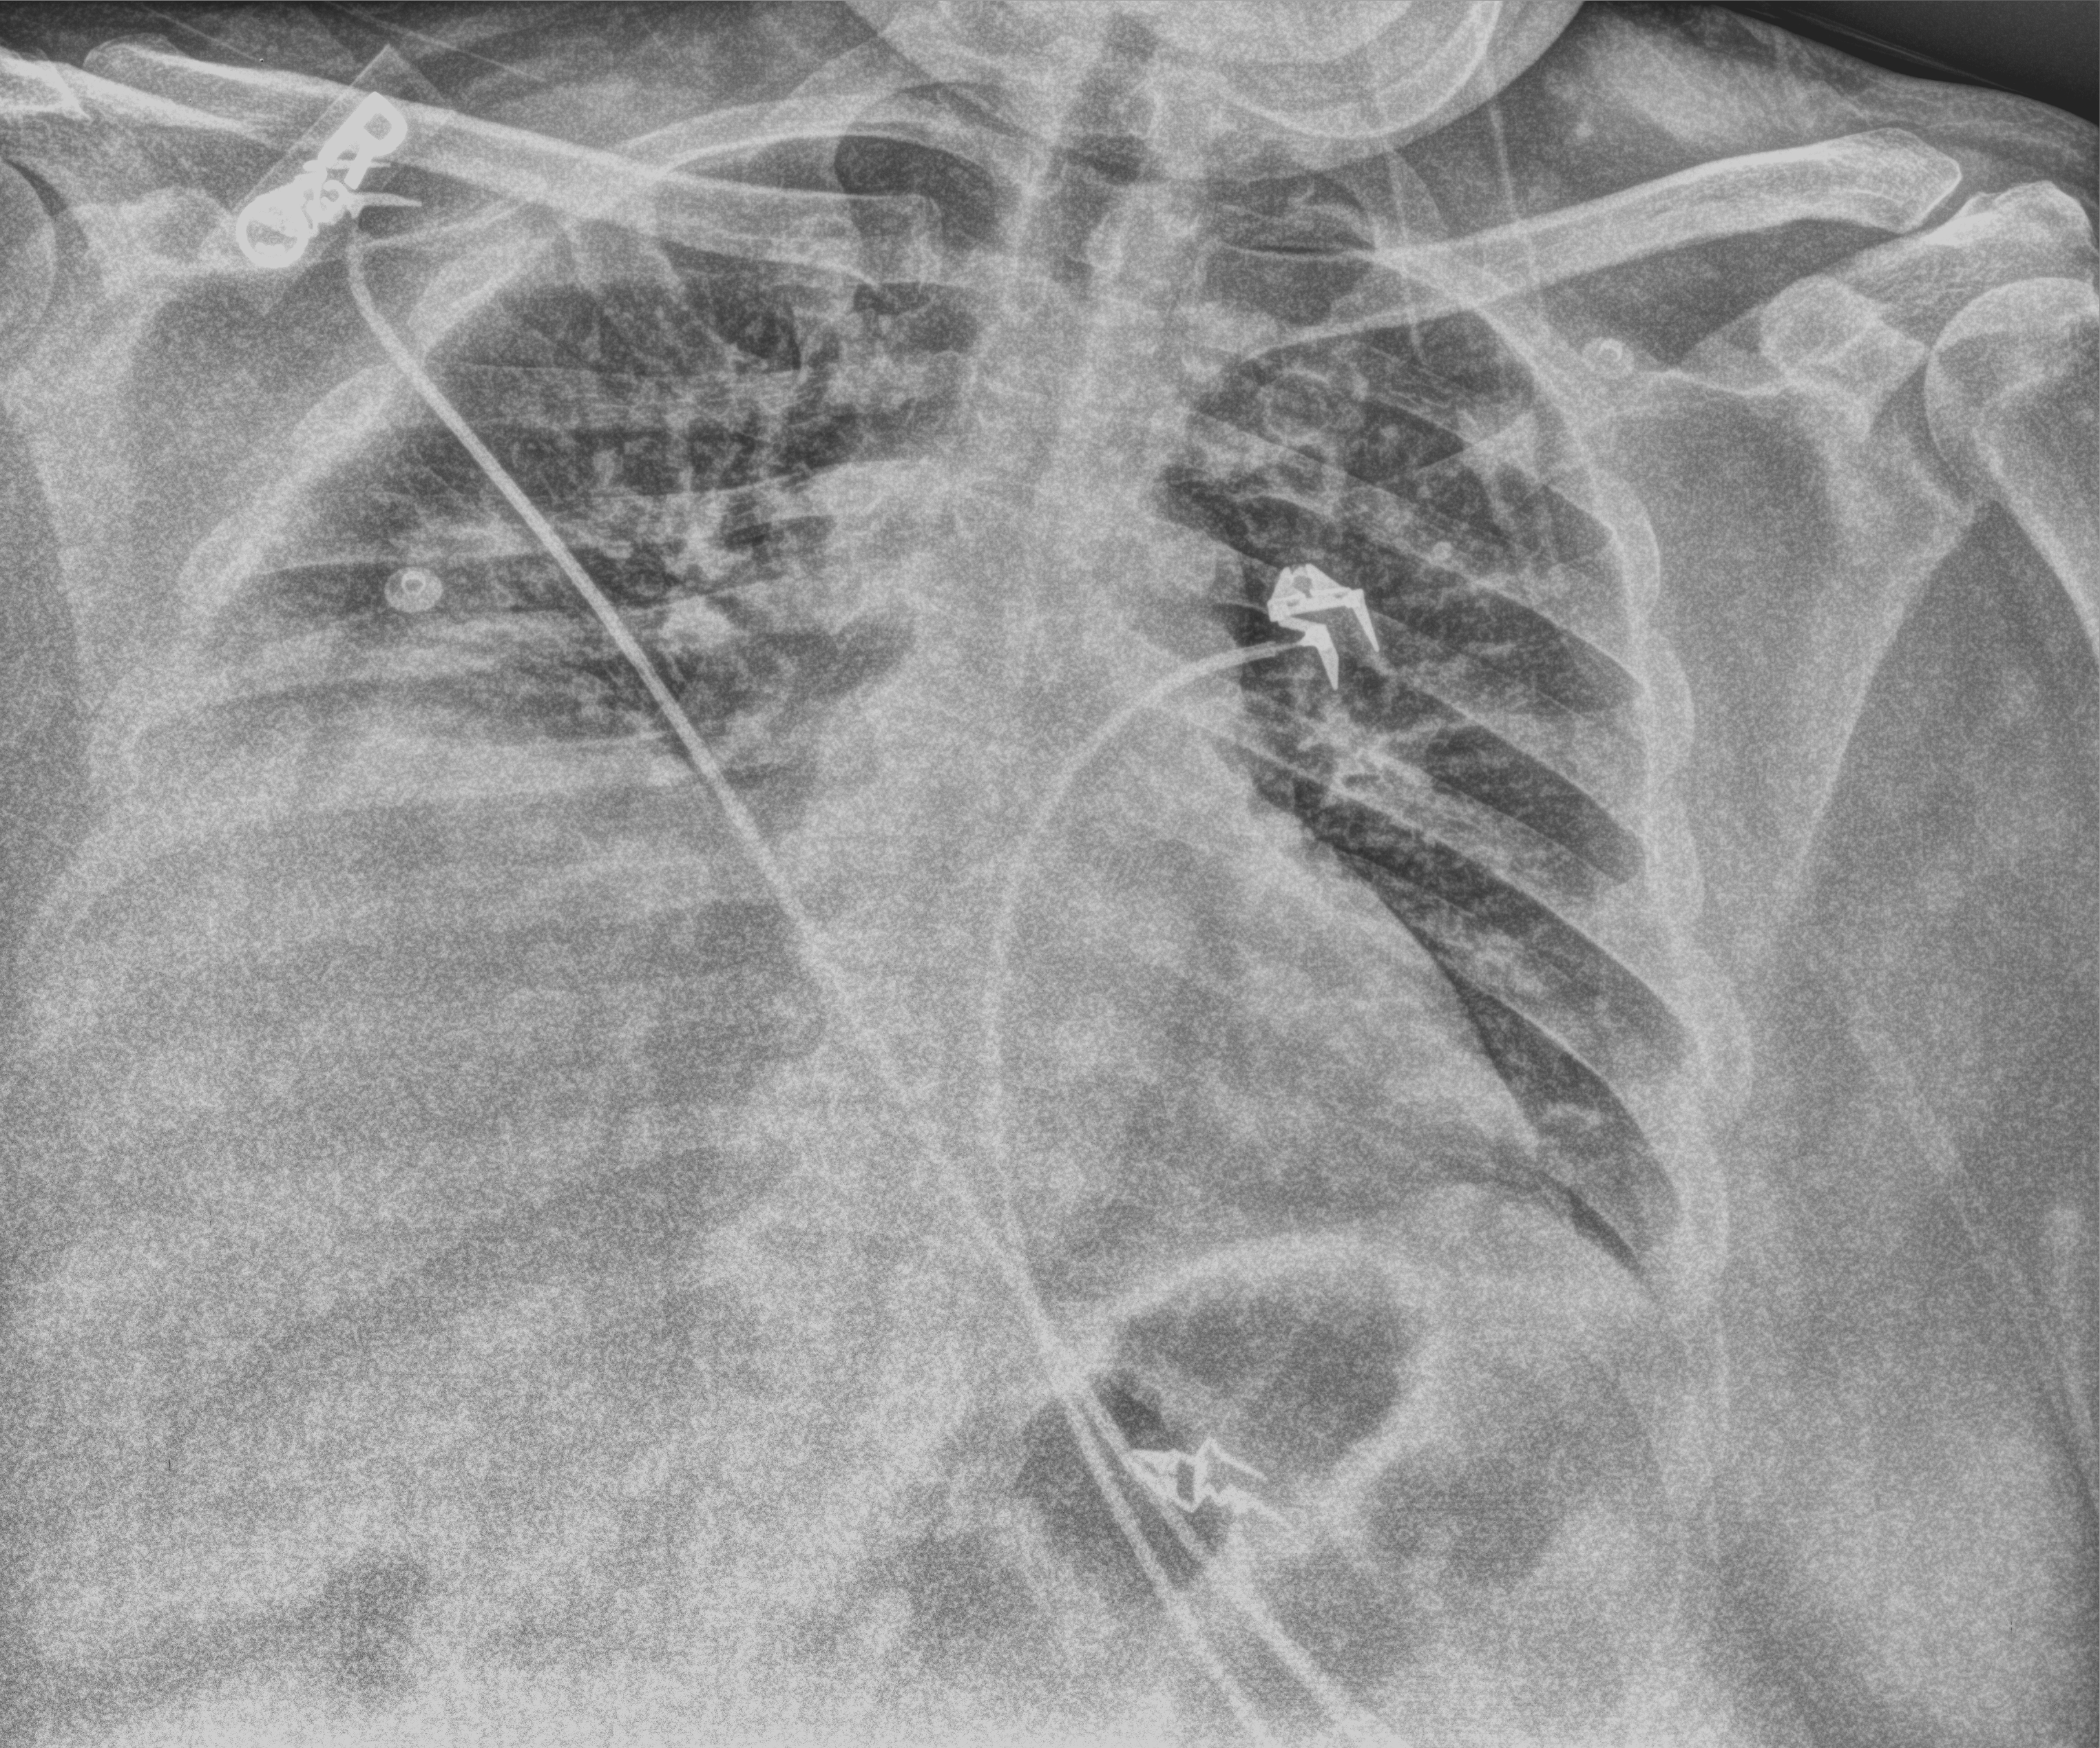
Portable chest radiograph. Patient hospitalised with COVID-19; male, aged 18–59 years.
Hospital-stay facts (about this admission, not read from this image; timing relative to this image not recorded): admitted to intensive care during this hospital stay: no; mechanically ventilated during this hospital stay: no.